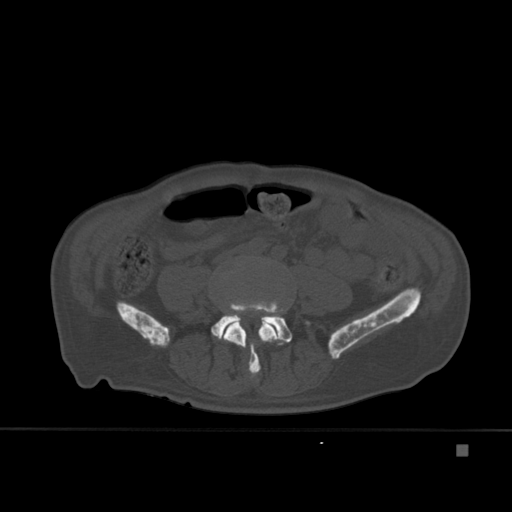
CT including the spine, one axial slice; position 113 of 451 along the scan axis; bone window (W 1800 / L 400 HU); 512 × 512 image matrix. Patient: male, 75 years. From the clinical record (not read from this slice): primary cancer: prostate.
Annotated regions visible in this slice (semi-automatic segmentation, software-assisted and operator-edited):
- L4 vertebra: bounding box (x1, y1, x2, y2) in pixels: (223, 300, 279, 378)
- L5 vertebra: (211, 300, 310, 345)
- T7 vertebra: (266, 309, 284, 324)